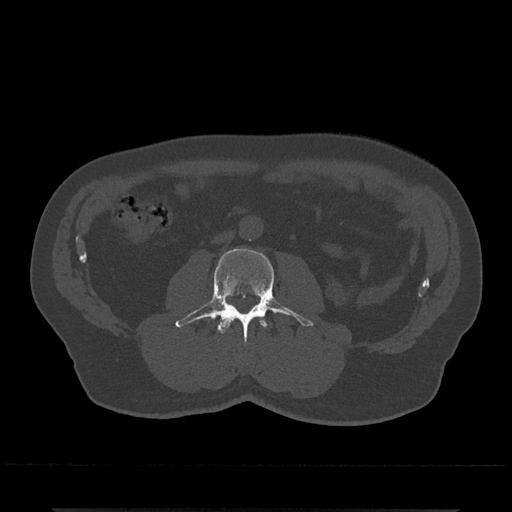
CT including the spine, one axial slice; slice 226 of 797 in the series (ordered by position); reconstruction kernel Br40s/3; bone window (W 1800 / L 400 HU); 0.5 mm slice thickness; 512 × 512 image matrix, field of view 393 × 393 mm. Patient: male, 67 years. From the clinical record (not read from this slice): primary cancer: prostate.
Structures marked on this image (semi-automatic segmentation, software-assisted and operator-edited):
- L2 vertebra: bounding box (x1, y1, x2, y2) in pixels: (218, 318, 267, 334)
- L3 vertebra: (175, 248, 313, 341)